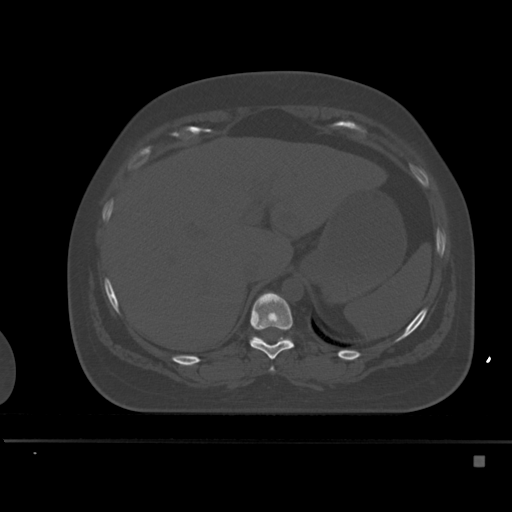
CT including the spine, one axial slice. Slice 245 of 495 in the series (ordered by position). Bone window (W 1800 / L 400 HU). 1.5 mm slice thickness. 512 × 512 image matrix, field of view 404 × 404 mm. Patient: female, 33 years. Case-level facts recorded for this patient, not image findings: primary cancer: breast; vertebrae with lytic lesions (as recorded): T1.
Outlined on this slice (semi-automatic segmentation, software-assisted and operator-edited):
- T10 vertebra: bounding box (x1, y1, x2, y2) in pixels: (250, 292, 294, 360)
- T11 vertebra: (251, 336, 290, 341)
- T9 vertebra: (270, 367, 275, 372)